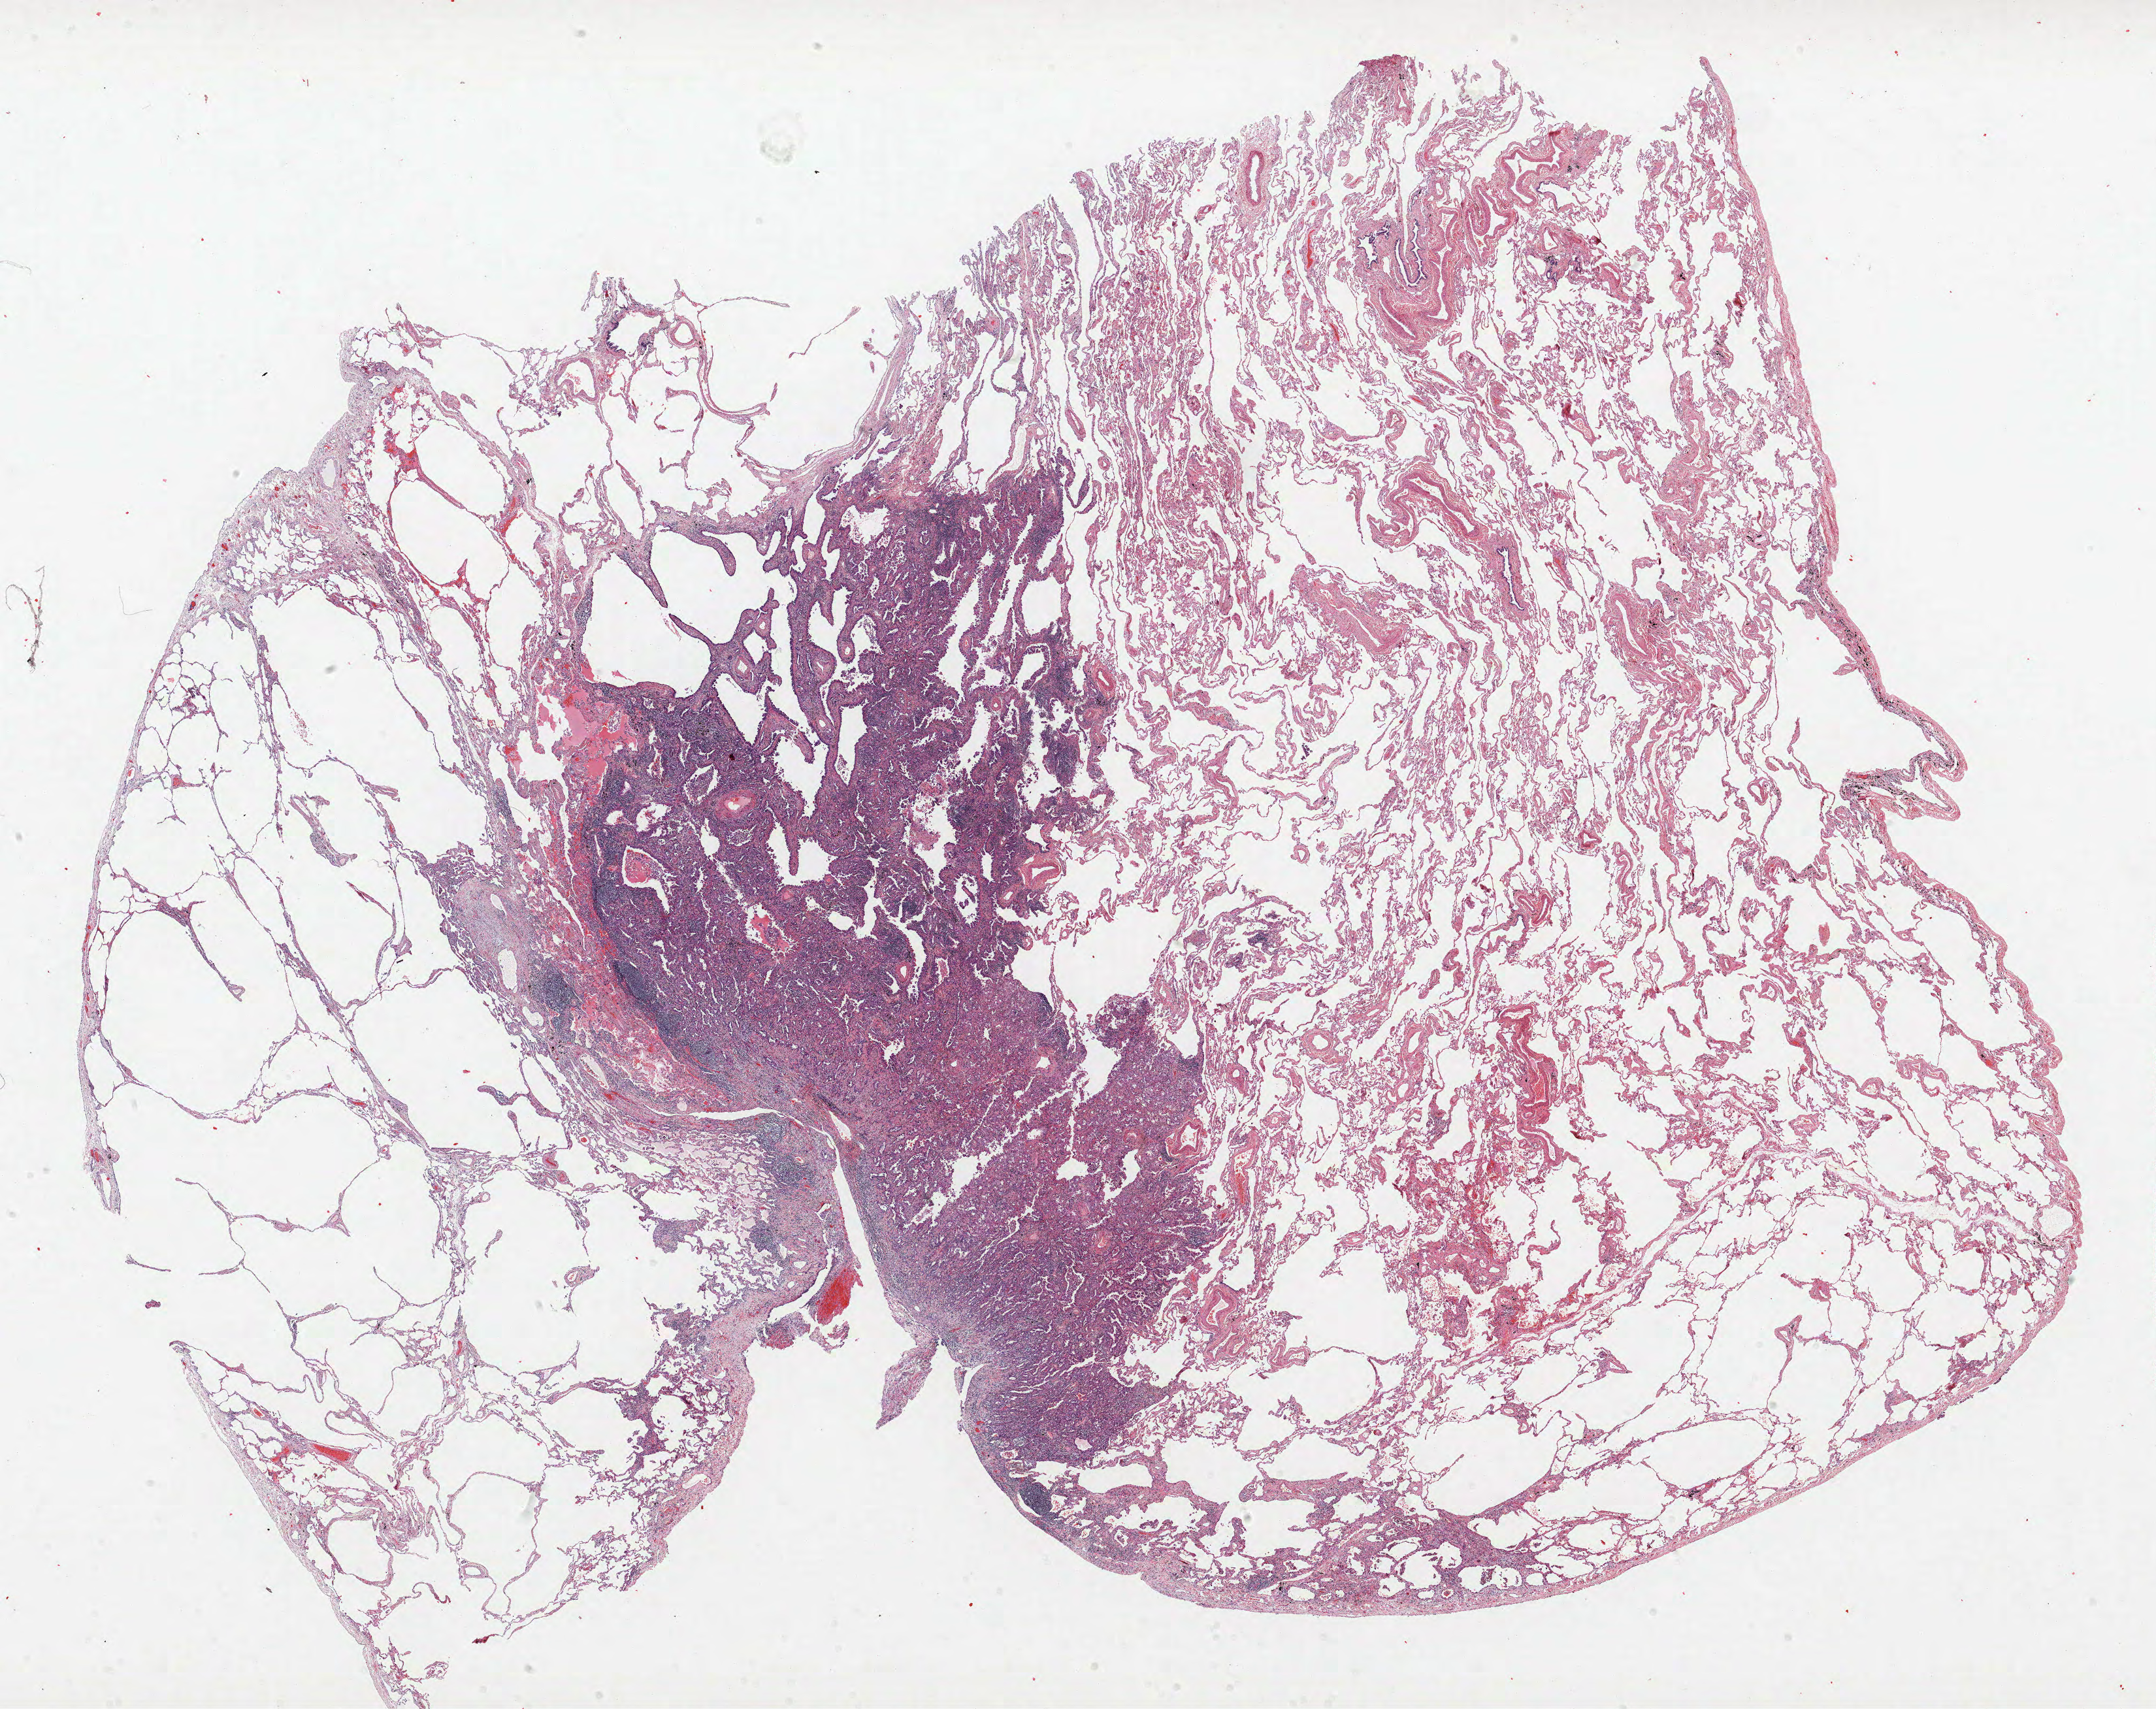
Whole-slide histology image, H&E-stained — low-resolution overview of the scanned area, about 26.4 x 20.9 mm, formalin-fixed paraffin-embedded (FFPE) section, lung. Male, age 65 at enrolment. Grade: moderately differentiated (G2).
Stage (AJCC 6th edition): IIA. Primary tumour location (clinical record): right upper lobe. Tumour size (pathology): 14 mm. Participant's lung-cancer diagnosis: Bronchiolo-alveolar adenocarcinoma, NOS.